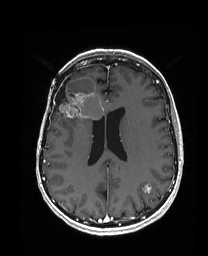
Brain MRI from a brain-tumour surgery series, one axial slice. Position 75 of 192 along the scan axis. T1-weighted post-contrast. 1 mm slice thickness. 208 × 256 image matrix. Case-level facts recorded for this patient, not image findings: histopathology: Metastatic Carcinoma from Breast primary; tumour location: Right Frontal.
Structures marked on this image (expert manual segmentation):
- previous resection cavity: bounding box [x1, y1, x2, y2] px = [54, 77, 70, 111]
- tumour: [55, 77, 104, 128]